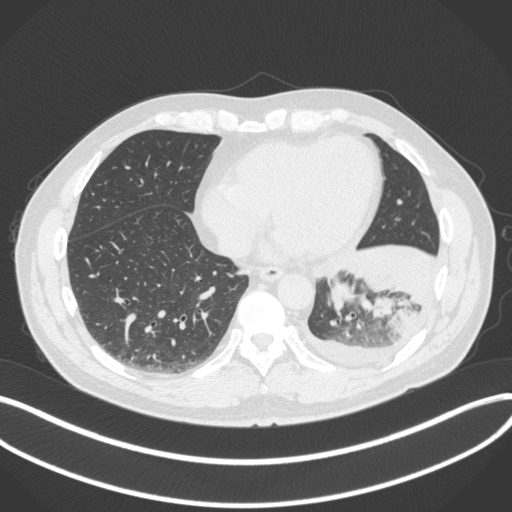
Chest CT, one axial slice; slice 110 of 350 in the series (ordered by position); reconstruction kernel B31f; lung window (W 1500 / L -600 HU); 1 mm slice thickness; 512 × 512 image matrix. Male patient, age 58 years. From the clinical record (not read from this slice): clinical TNM (as recorded): T3 N1 M1b.
Annotated regions visible in this slice (bounding box drawn by a radiologist):
- lung tumour (recorded histology: small cell carcinoma): bounding box <319,271,362,314> (left, top, right, bottom; pixels)